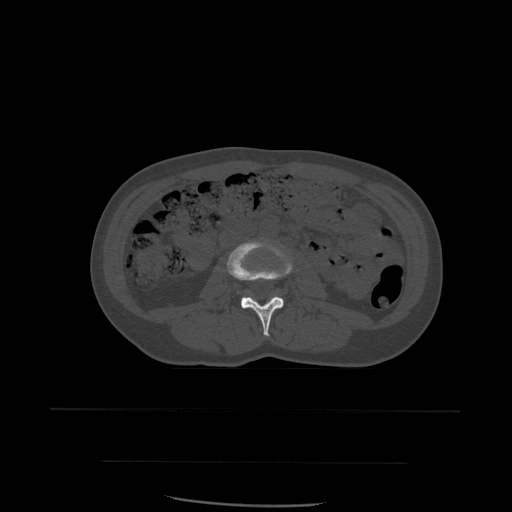
CT including the spine, one axial slice; position 191 of 574 along the scan axis; bone window (W 1800 / L 400 HU); 1.25 mm slice thickness; 512 × 512 image matrix, field of view 392 × 392 mm. Patient age 48 years. From the clinical record (not read from this slice): primary cancer: lung; vertebrae with lytic lesions (as recorded): T11.
Structures marked on this image (semi-automatically segmented with operator editing):
- L3 vertebra: bounding box (x1, y1, x2, y2) in pixels: (227, 241, 294, 337)